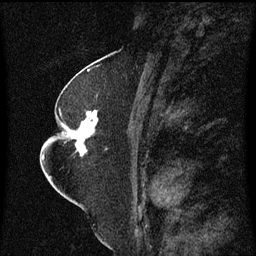
Breast MRI (dynamic contrast-enhanced), one sagittal slice. Slice 32 of 60 in the series (ordered by position). Dynamic contrast-enhanced series, image 2 of 3 at this slice position (ordered by acquisition). 1.5 T. TE 4.2 ms, TR 8.4 ms. 2 mm slice thickness. 256 × 256 image matrix. Patient: female, 52 years. From the clinical record (not read from this slice): setting: breast cancer imaged before/during neoadjuvant chemotherapy; receptor status: HR-positive, HER2-negative.
Annotated regions visible in this slice (semi-automatically segmented with operator editing):
- analysis volume of interest (the breast-tissue region the enhancement analysis was run in; not a lesion): bounding box [x1, y1, x2, y2] px = [64, 110, 109, 157]
- tumour enhancement mask (voxels above the 70 % enhancement threshold inside the analysis volume of interest): [72, 112, 99, 157]